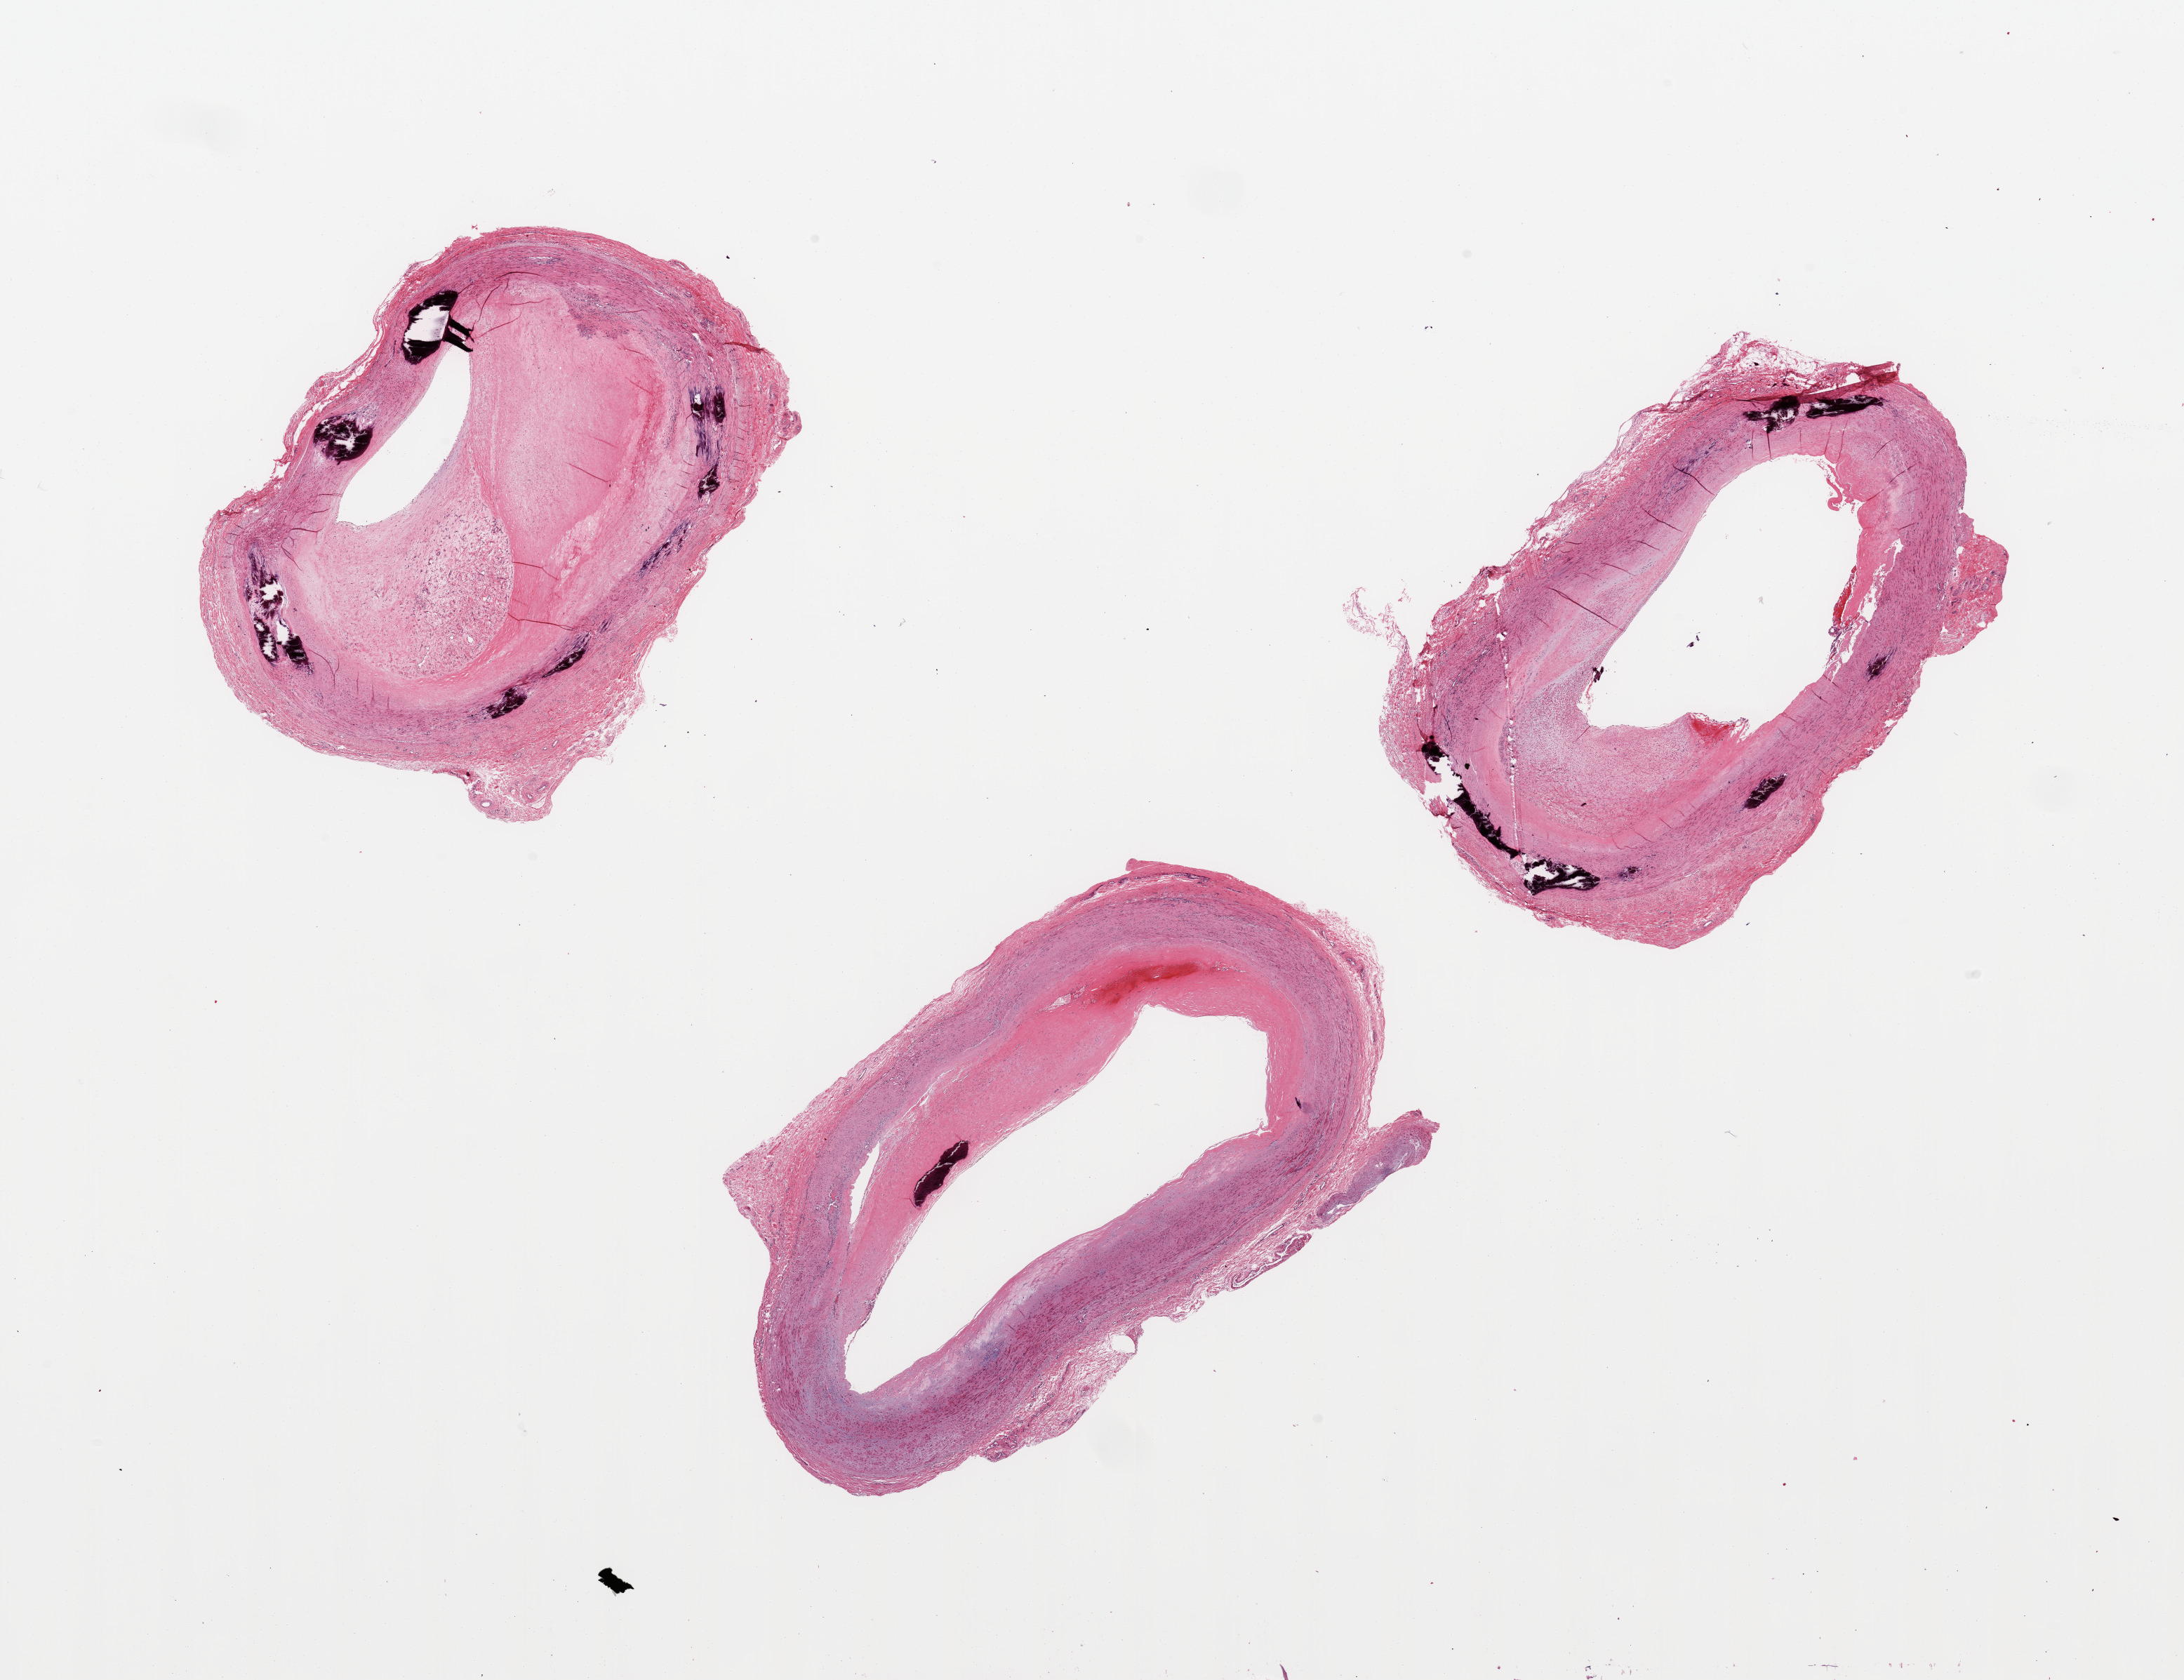
Hematoxylin and eosin (H&E) whole-slide image, a low-resolution overview of the entire scanned area, about 24.6 x 18.9 mm. PAXgene-fixed paraffin-embedded (PFPE) section. Target tissue: tibial artery. Tissue donor sample. Donor: male.
• pathologist's review note for this sample: 3 pieces; severe intimal sclerosis and mainly medial calcification; well trimmed